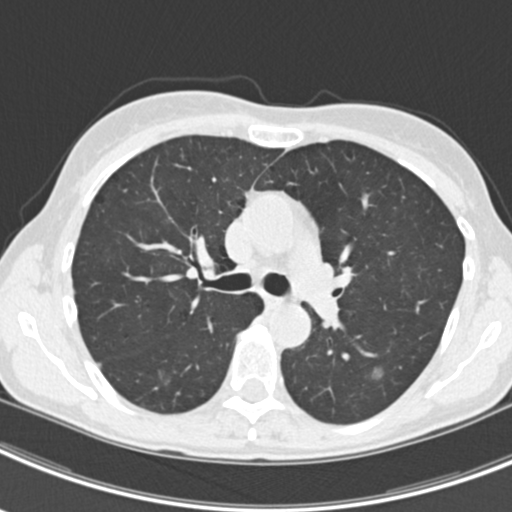
Chest CT (low-dose screening protocol), one axial image; second annual screen; lung window (W 1500 / L -600 HU); standard (soft-tissue) reconstruction kernel (B30f); 120 kVp; slice 73 of 219 in the series; 512 × 512 image matrix, field of view 298 × 298 mm. Female participant, aged 63 years at enrolment. Current smoker at enrolment.
2 expert reader's lesion annotations on this slice (largest first), bounding box (x1, y1, x2, y2) in pixels: (364, 356, 405, 392); (144, 361, 177, 395). The screening reader recorded 9 non-calcified nodules or masses ≥4 mm on this exam (left upper lobe, right upper lobe, left upper lobe, left lower lobe, right middle lobe, left lower lobe, left lower lobe, right lower lobe, right lower lobe); which of them these boxes mark is not recorded. Official screen result: positive, other. Participant outcome: lung cancer diagnosed 408 days after this screen (after the third annual screen) — bronchiolo-alveolar adenocarcinoma, NOS, right upper lobe, right middle lobe, right lower lobe, left upper lobe, left lower lobe, moderately differentiated (G2), stage IV (AJCC 6th edition).